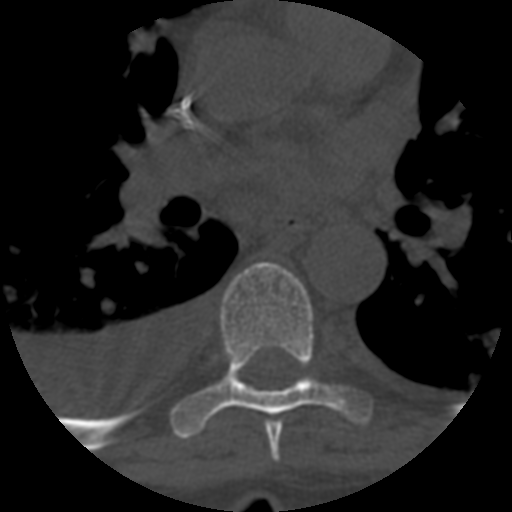
CT including the spine, one axial slice; slice 418 of 708 in the series (ordered by position); reconstruction kernel STANDARD; 120 kVp; one of 3 acquisitions stored at this slice position; bone window (W 1800 / L 400 HU); 512 × 512 image matrix, field of view 160 × 160 mm. Patient age 55 years. From the clinical record (not read from this slice): primary cancer: colon; vertebrae with lytic lesions (as recorded): T12, L1, L5.
Annotated regions visible in this slice (semi-automatic segmentation, software-assisted and operator-edited):
- T6 vertebra: bounding box <265,421,283,462> (left, top, right, bottom; pixels)
- T7 vertebra: <172,262,372,439>